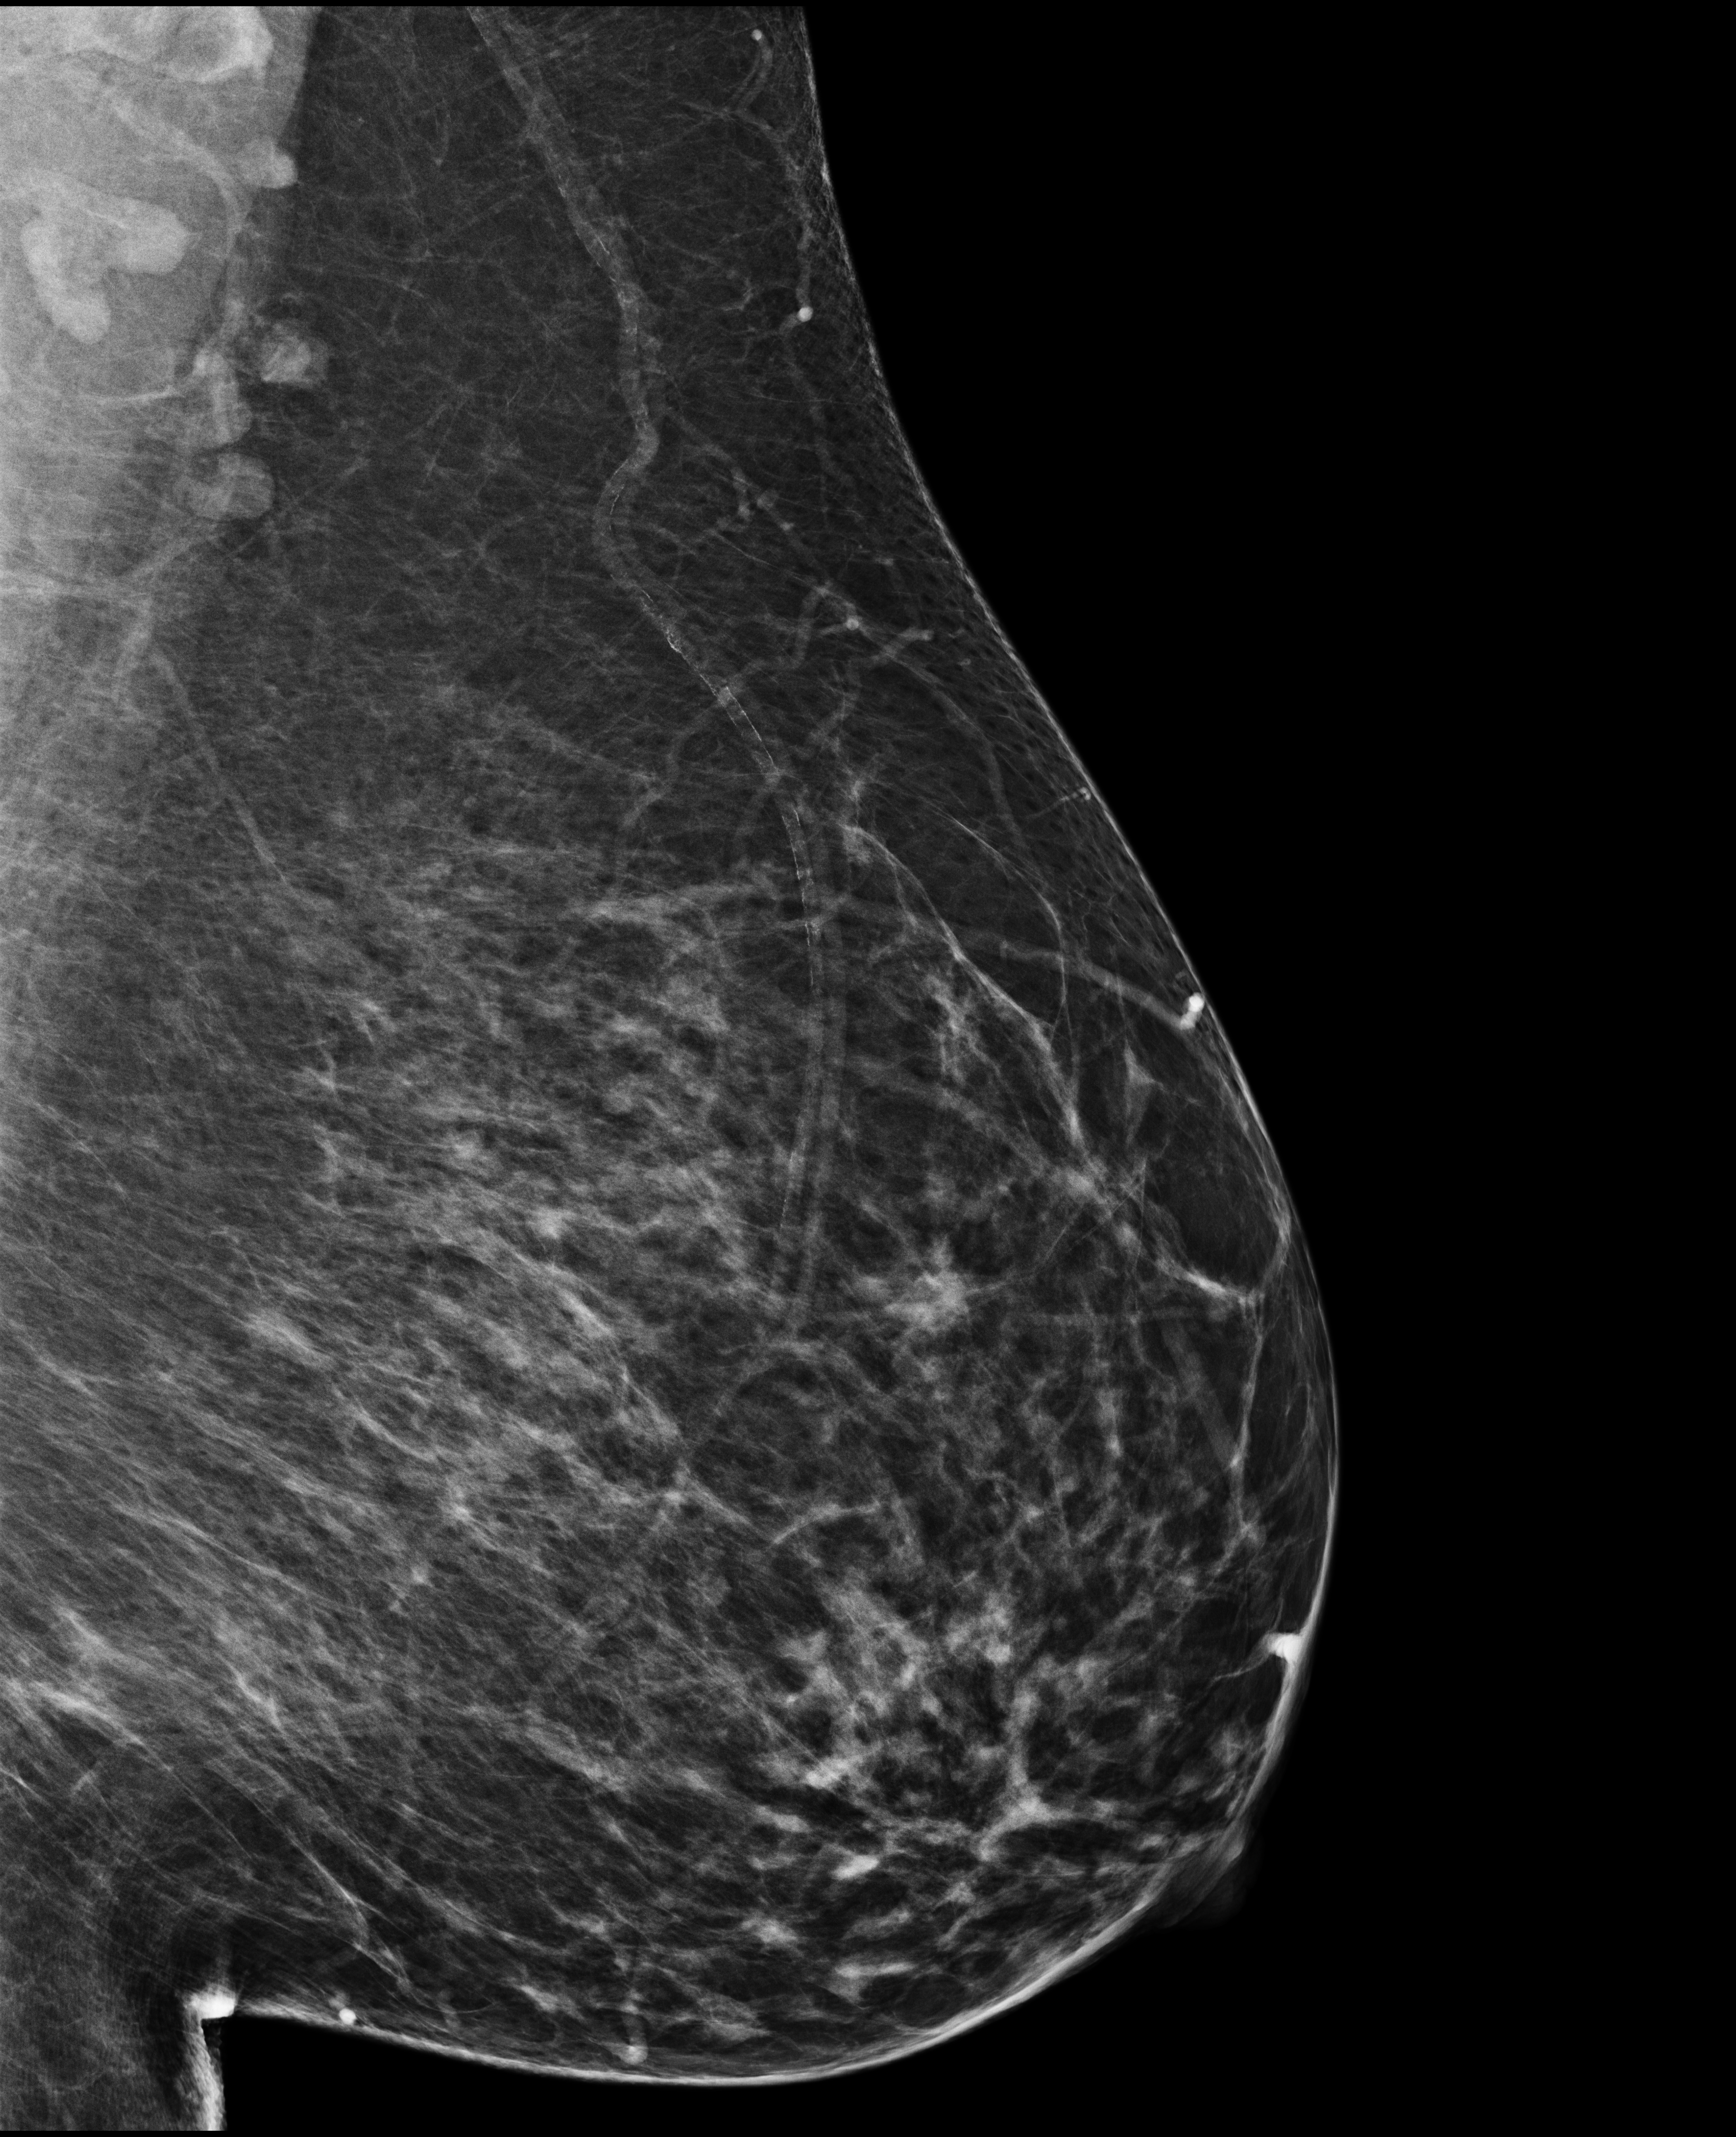
Annual screening mammography examination, system: Selenia Dimensions. Patient: female, 68 years.
Image type: full-field digital mammogram. Breast: left. Projection: MLO view.